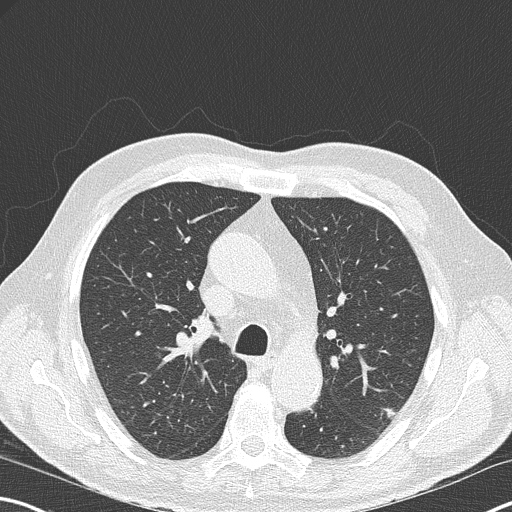
Low-dose screening chest CT, axial slice. Second annual screen. Lung window (W 1500 / L -600 HU). 2 mm slice thickness. 120 kVp. Slice 74 of 178 in the series. 512 × 512 image matrix. Male participant, aged 67 years at enrolment. Former smoker at enrolment.
Expert reader's lesion annotation, box from (x=370, y=394) to (x=410, y=429) px. Reader record for this screening exam (exam-level; its link to the box is not recorded): non-calcified nodule or mass ≥4 mm, left upper lobe, 9 × 6 mm, poorly defined margins, soft tissue attenuation, pre-existing on the prior screen: no. Official screen result: positive, other.